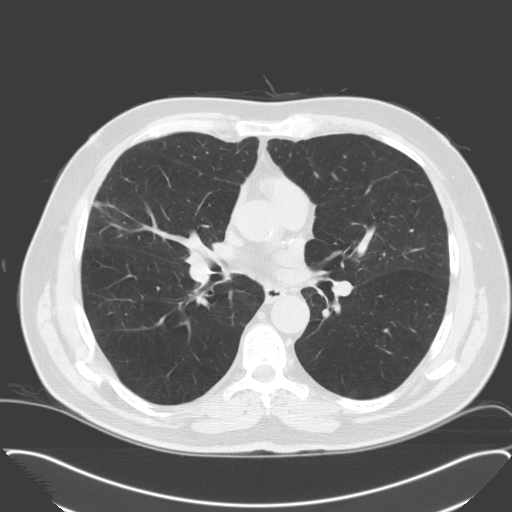
Low-dose screening chest CT, one axial slice. Slice 96 of 174 in the series (ordered by position). 120 kVp. Lung window (W 1500 / L -600 HU). 3.2 mm slice thickness. 512 × 512 image matrix.
Outlined on this slice (outlined manually by an expert reader):
- lesion 1 (tumor, middle lobe of right lung): bounding box <93,201,102,209> (left, top, right, bottom; pixels)